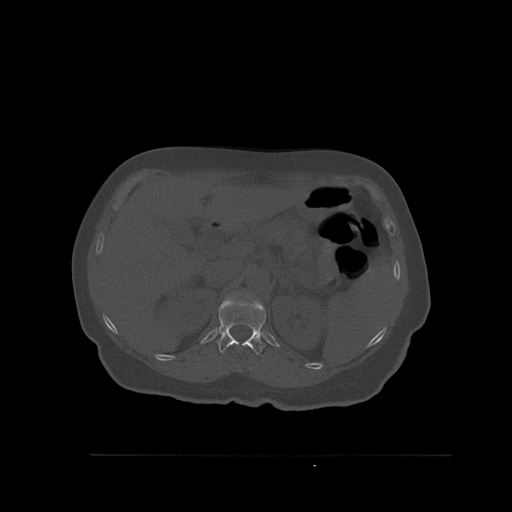
CT including the spine, one axial slice. Bone window (W 1800 / L 400 HU). 1.5 mm slice thickness. 512 × 512 image matrix, field of view 470 × 470 mm. Female patient, age 73 years. Case-level facts recorded for this patient, not image findings: primary cancer: breast.
Structures marked on this image (semi-automatic segmentation, software-assisted and operator-edited):
- T12 vertebra: bounding box (x1, y1, x2, y2) in pixels: (216, 297, 266, 355)